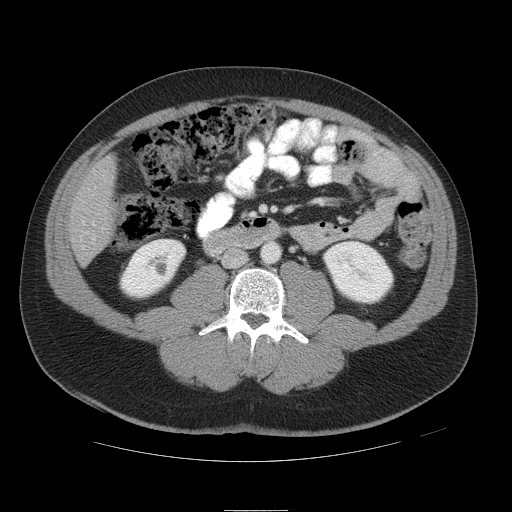
Contrast-enhanced abdominal CT, one axial slice. Position 13 of 49 along the scan axis. Reconstruction kernel STANDARD. Intravenous contrast given. Soft-tissue window (W 400 / L 40 HU). 5 mm slice thickness. 512 × 512 image matrix, field of view 425 × 425 mm. Male patient, age 52 years. From the clinical record (not read from this slice): diagnosis: colorectal cancer liver metastases, imaged before liver resection; multiple liver metastases: yes; largest metastasis: 5.1 cm; disease in both lobes: yes.
Annotated regions visible in this slice (manually delineated by an expert):
- liver: bounding box <70,159,116,262> (left, top, right, bottom; pixels)